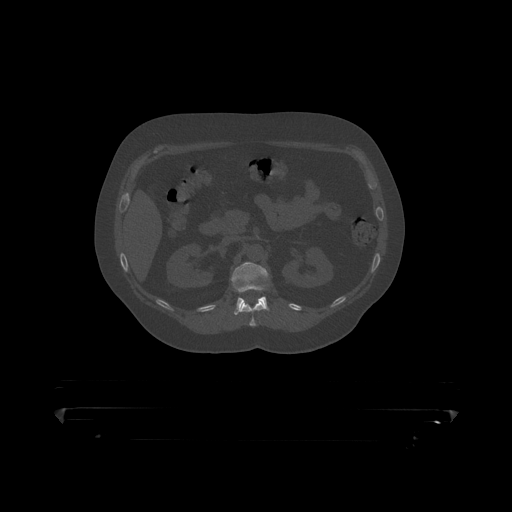
CT including the spine, one axial slice; slice 157 of 390 in the series (ordered by position); reconstruction kernel STANDARD; bone window (W 1800 / L 400 HU); 1.25 mm slice thickness; 512 × 512 image matrix, field of view 650 × 650 mm. Patient: male, 60 years. From the clinical record (not read from this slice): primary cancer: prostate.
Annotated regions visible in this slice (semi-automatically segmented with operator editing):
- L1 vertebra: bounding box [x1, y1, x2, y2] px = [232, 262, 269, 315]
- T12 vertebra: [240, 300, 267, 319]